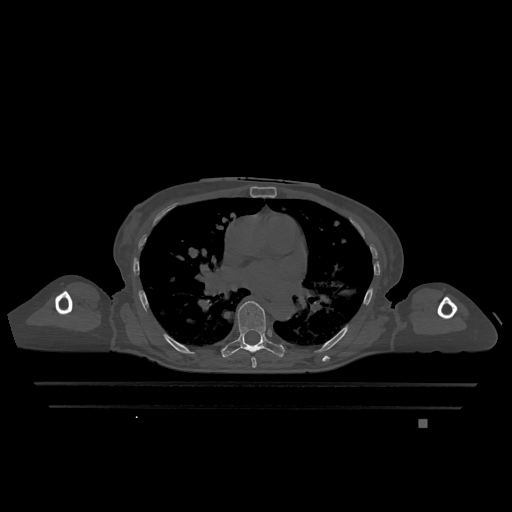
CT including the spine, one axial slice. Bone window (W 1800 / L 400 HU). 512 × 512 image matrix, field of view 500 × 500 mm. Patient: female, 74 years. From the clinical record (not read from this slice): primary cancer: lung; vertebrae with lytic lesions (as recorded): T1, T4, T5, T6, L4, L5.
Structures marked on this image (semi-automatically segmented with operator editing):
- T6 vertebra: box from (x=251, y=357) to (x=257, y=368) px
- T7 vertebra: (x=221, y=301)–(x=285, y=358)